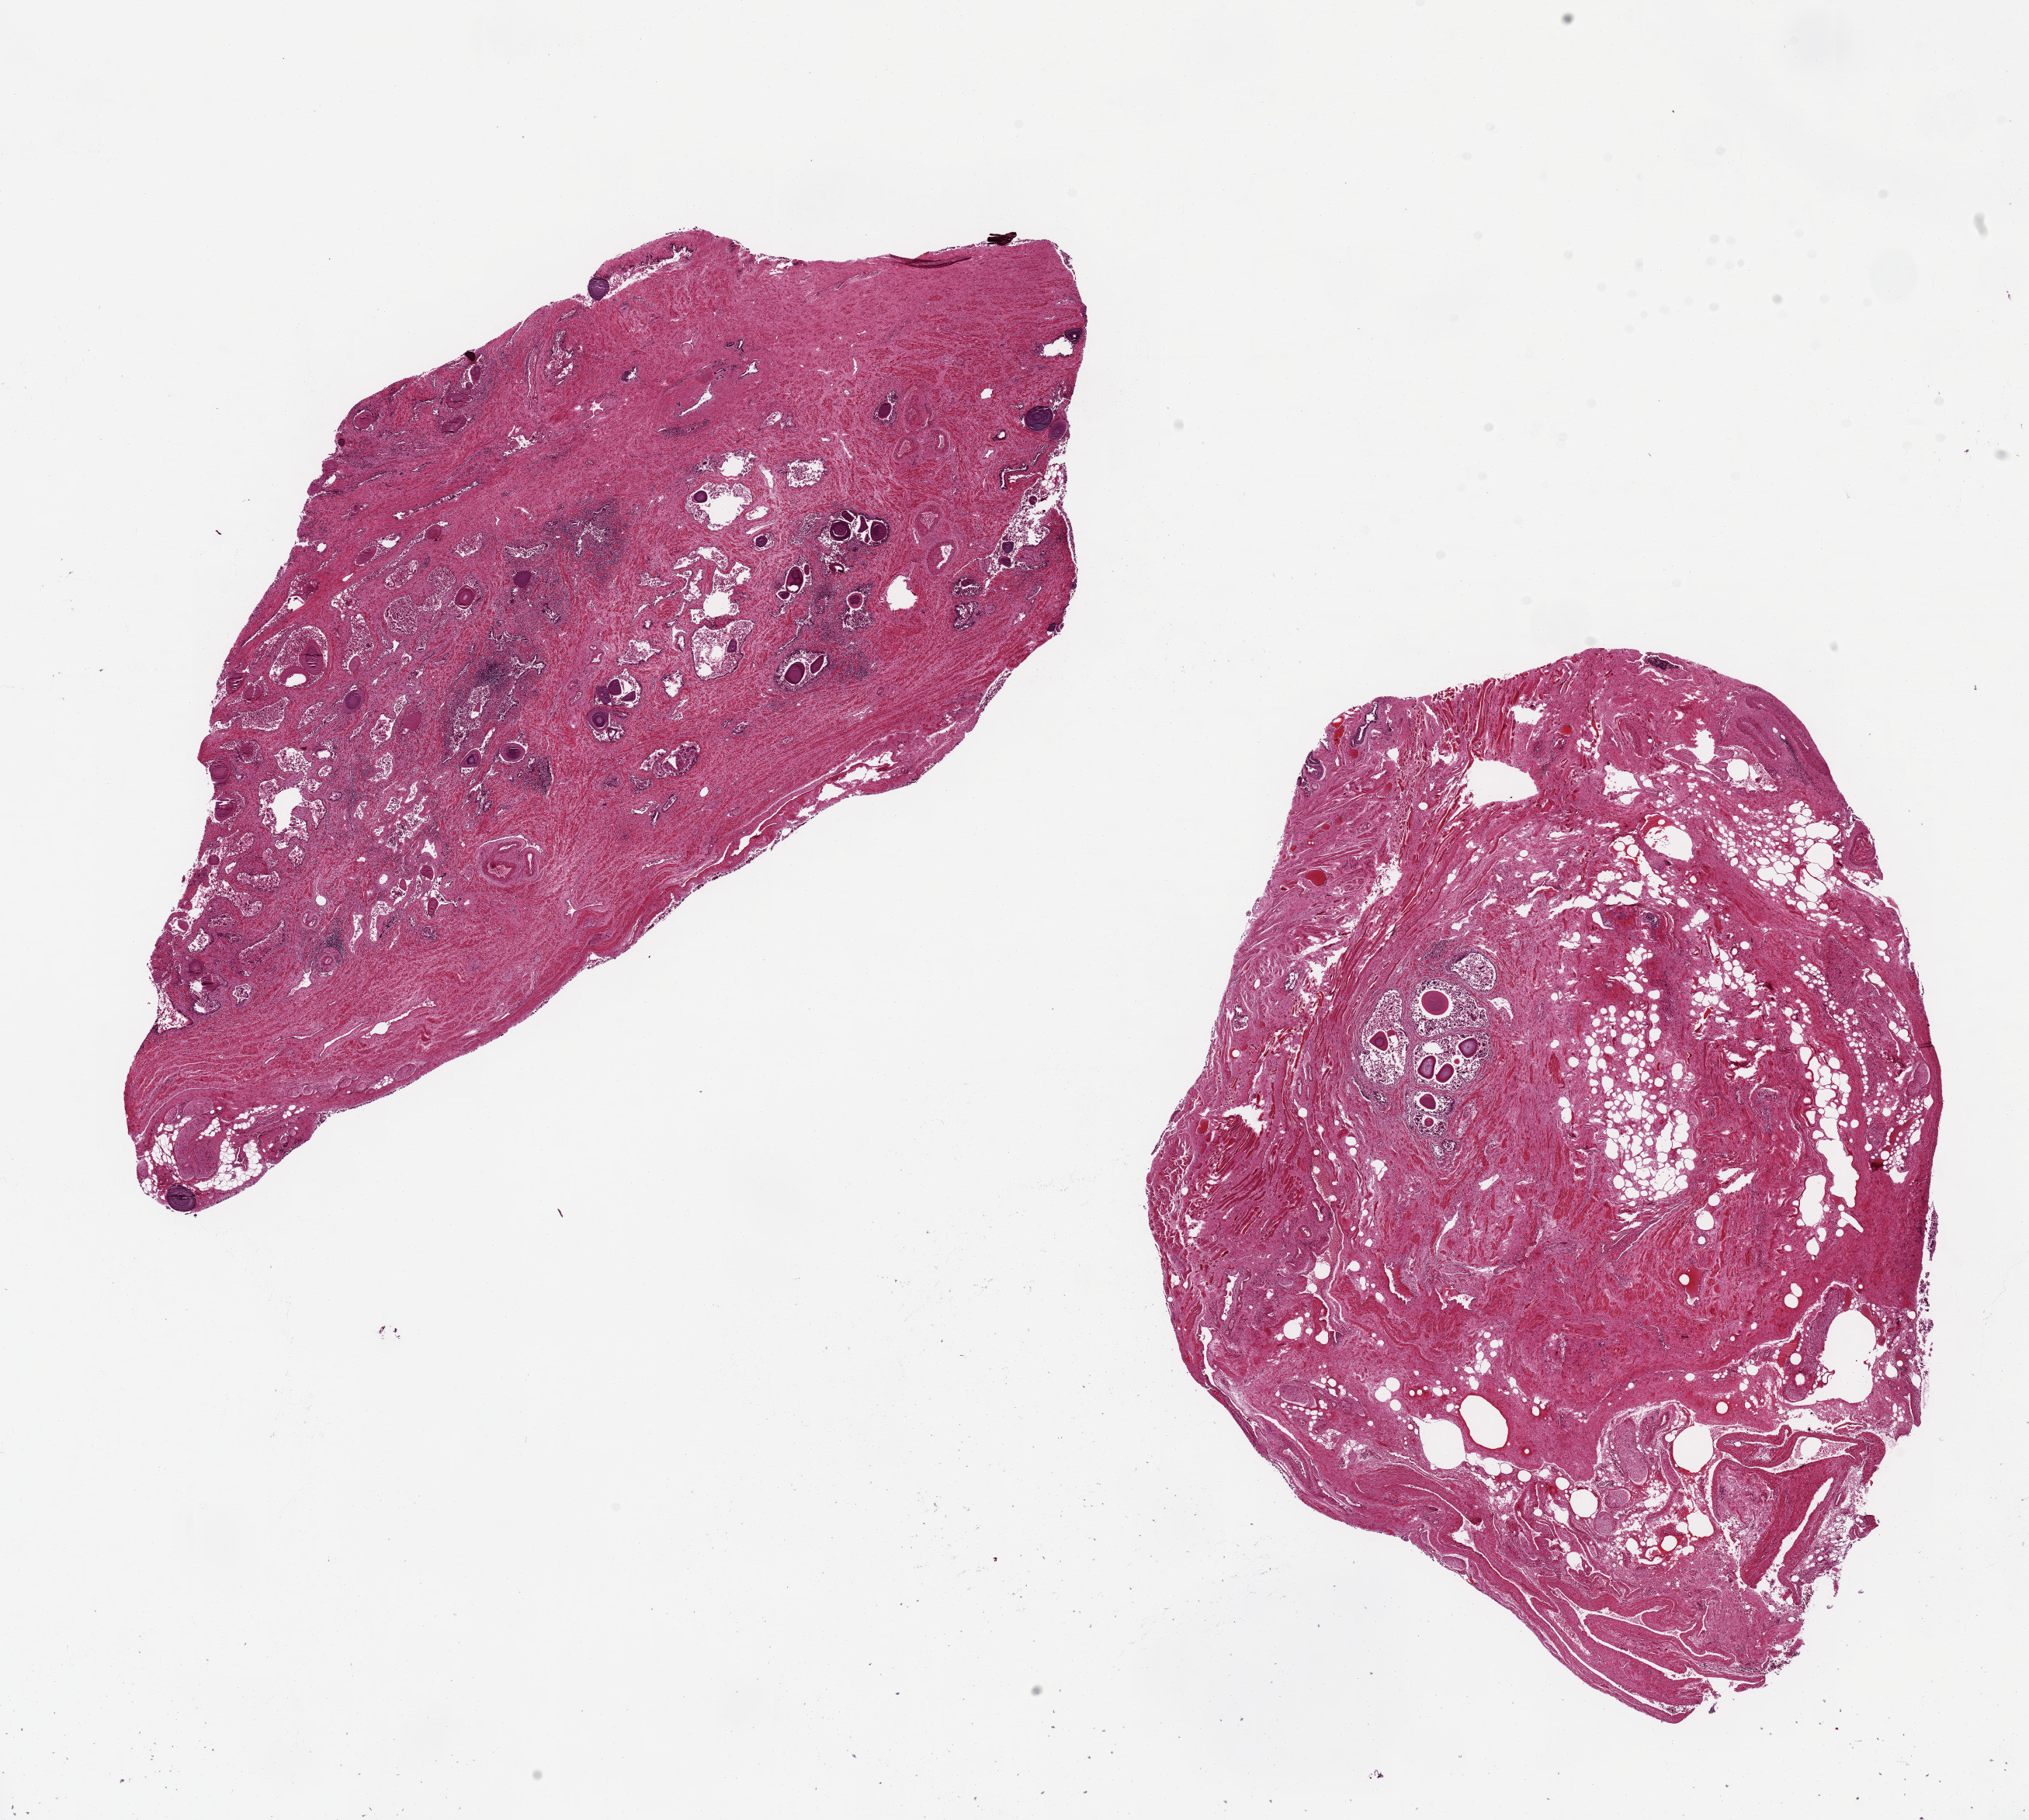
Digitized hematoxylin and eosin (H&E)-stained section — whole scanned area (about 20.7 x 18.5 mm) shown as a low-resolution overview, PAXgene-fixed, paraffin-embedded tissue, target tissue: prostate, donor tissue sample. Donor: male.
* reviewer comment on this tissue sample: 2 aliquots, ~10x7mm. Glands with near-total autolysis, patchy hyperplasia based on pattern, patchy chronic prostatitis